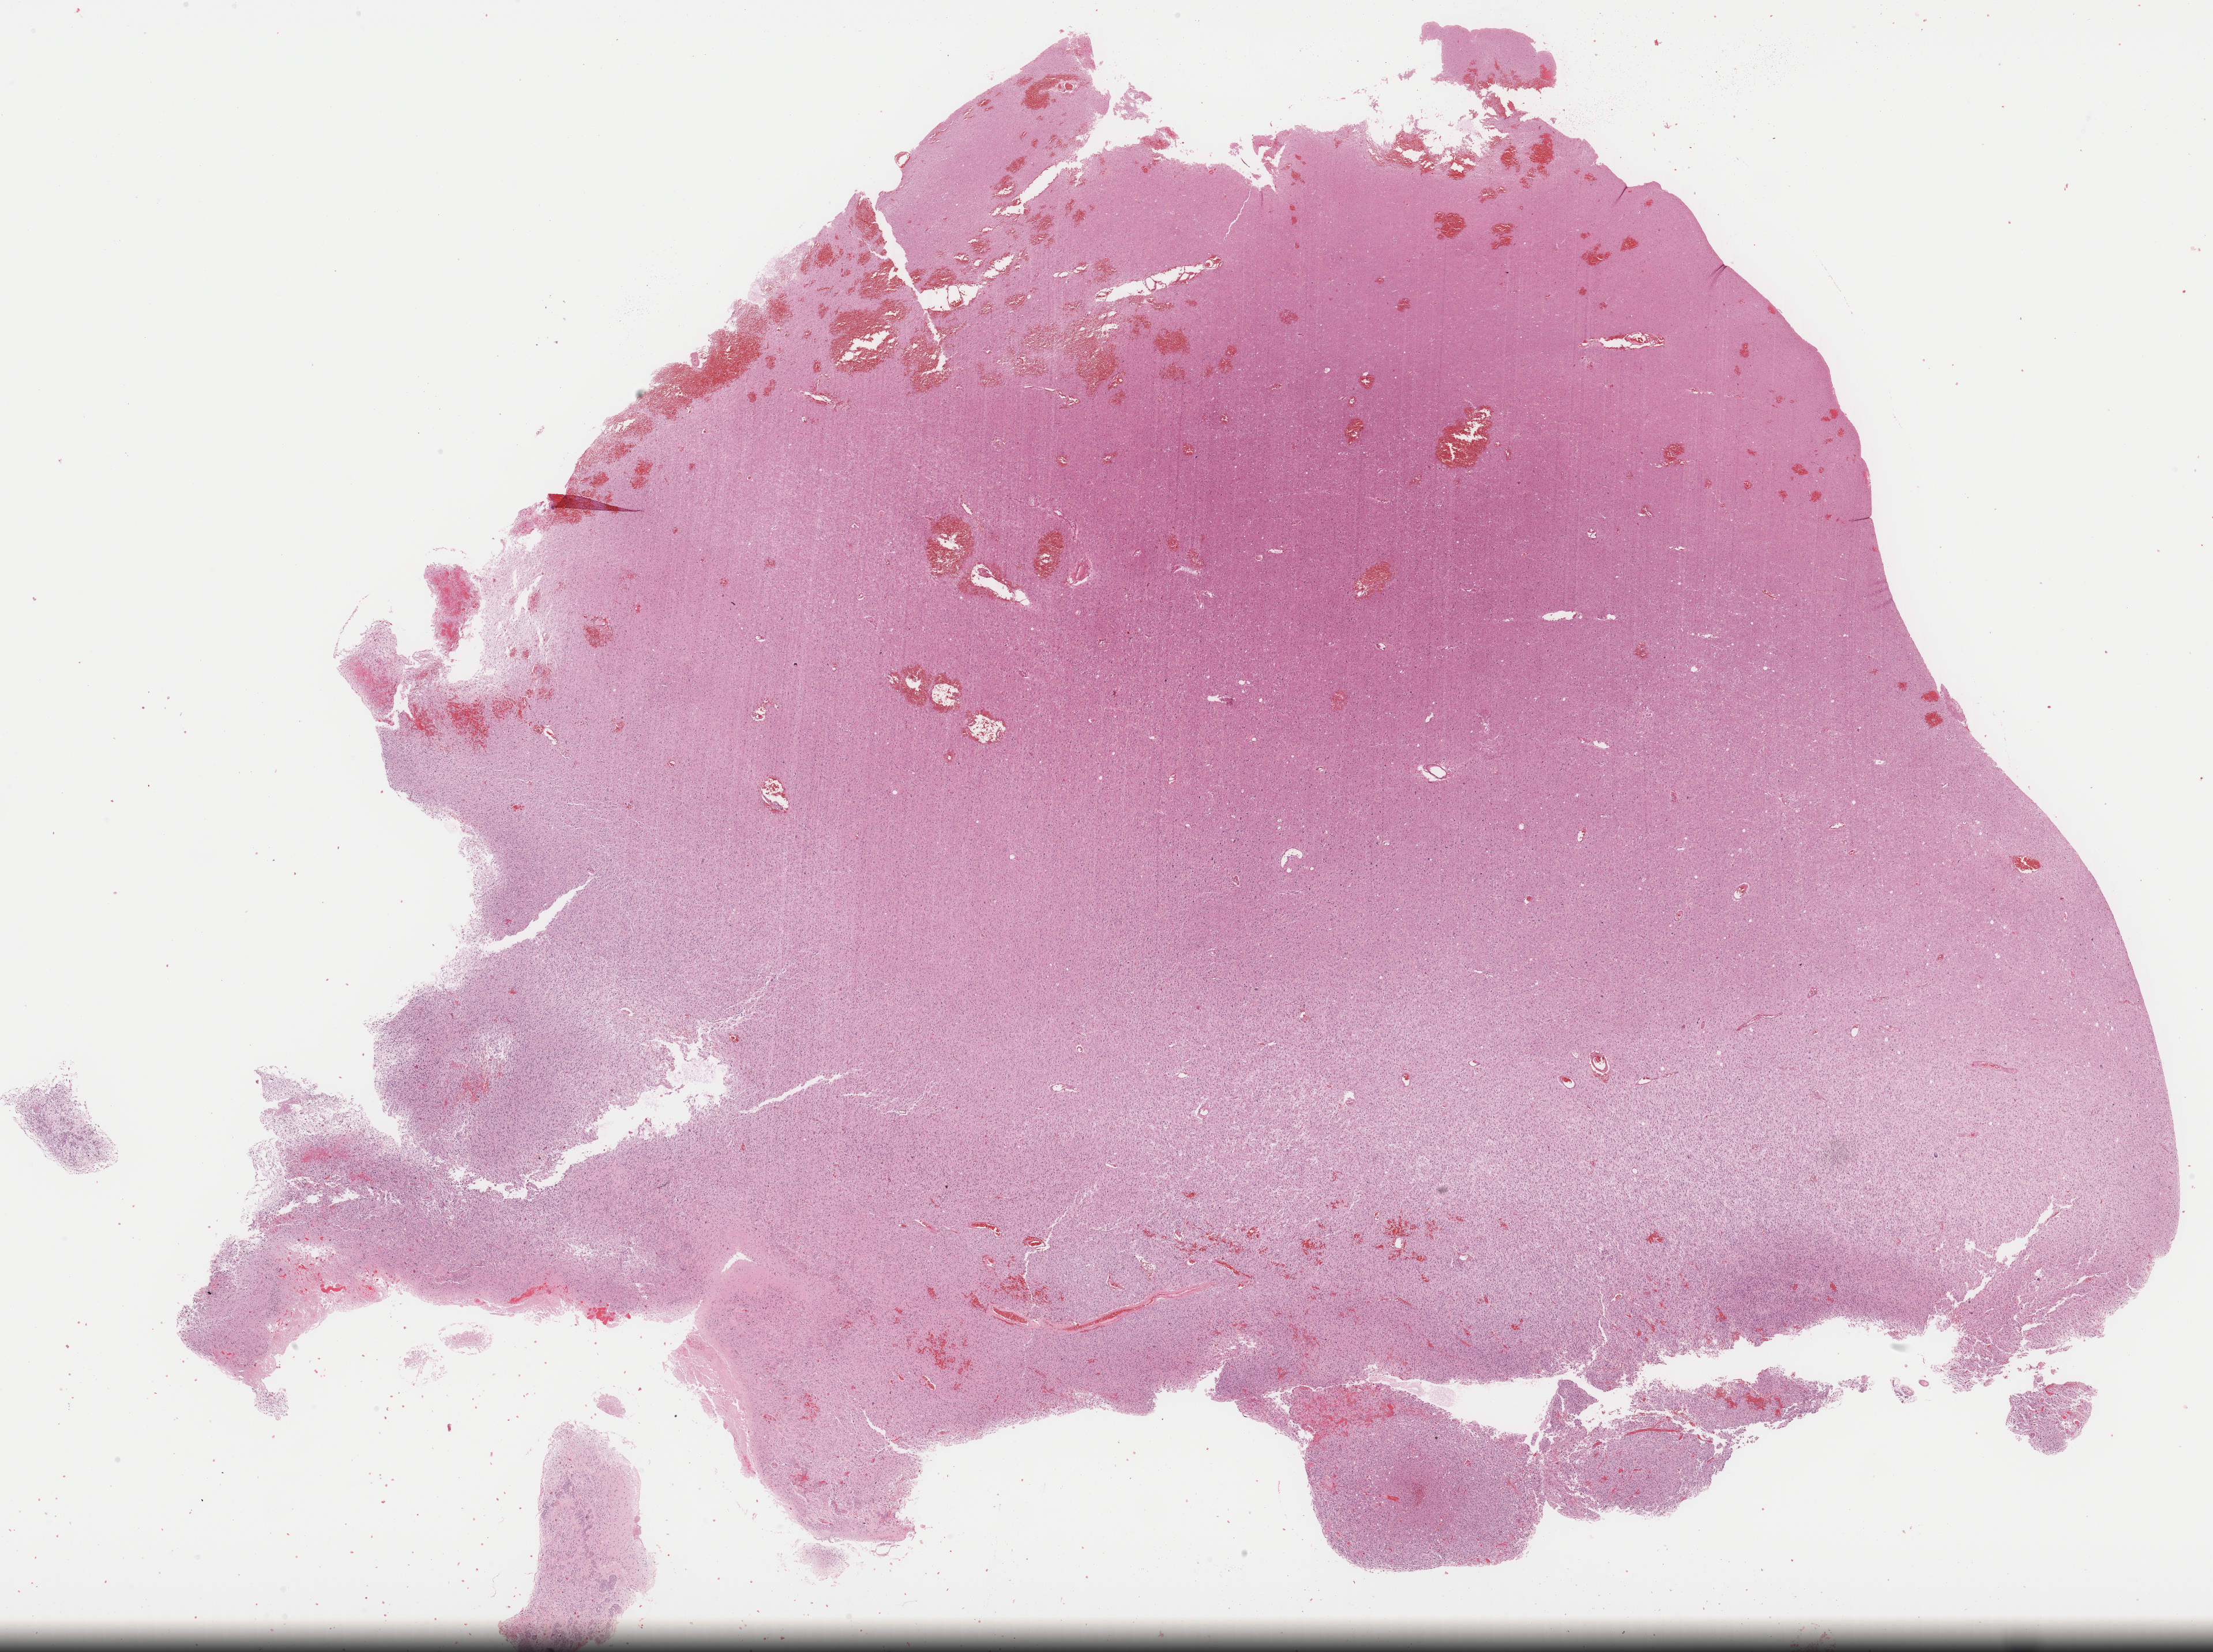
H&E-stained whole-slide image, a low-resolution overview of the entire scanned area, about 30.2 x 22.6 mm (from a 40x scan), formalin-fixed paraffin-embedded (FFPE) diagnostic section, primary tumour sample from the brain. Male, age 21 years at initial diagnosis.
• diagnosis: Glioblastoma